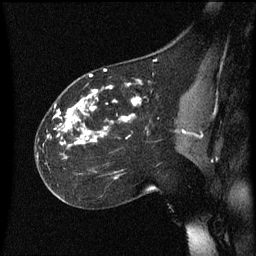
Breast MRI (dynamic contrast-enhanced), one sagittal slice. Slice 34 of 60 in the series (ordered by position). Dynamic contrast-enhanced series, image 2 of 3 at this slice position (ordered by acquisition). 1.5 T. TE 4.2 ms, TR 8.4 ms. 256 × 256 image matrix. Female patient, age 35 years. Case-level facts recorded for this patient, not image findings: setting: breast cancer imaged before/during neoadjuvant chemotherapy; receptor status: HER2-positive.
Outlined on this slice (semi-automatically segmented with operator editing):
- analysis volume of interest (the breast-tissue region the enhancement analysis was run in; not a lesion): bounding box [x1, y1, x2, y2] px = [36, 72, 178, 173]
- tumour enhancement mask (voxels above the 70 % enhancement threshold inside the analysis volume of interest): [48, 74, 142, 145]